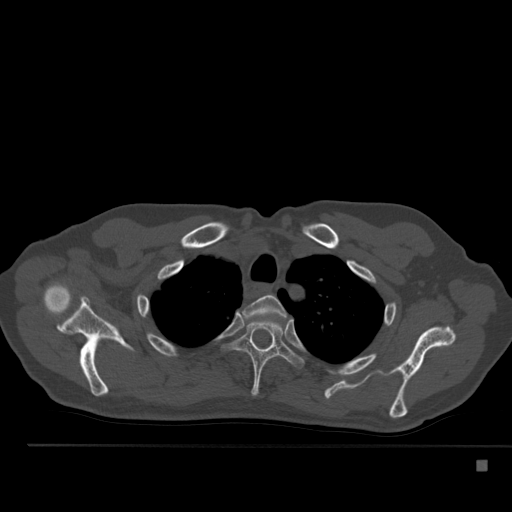
CT including the spine, one axial slice. Slice 400 of 517 in the series (ordered by position). Reconstruction kernel Br40s. Bone window (W 1800 / L 400 HU). 512 × 512 image matrix. Patient: male, 70 years. Case-level facts recorded for this patient, not image findings: primary cancer: renal; vertebrae with lytic lesions (as recorded): T4, T6, T10, T12, L3, L4, L5.
Outlined on this slice (semi-automatic segmentation, software-assisted and operator-edited):
- T2 vertebra: bounding box <244,295,290,320> (left, top, right, bottom; pixels)
- T3 vertebra: <227,321,304,397>